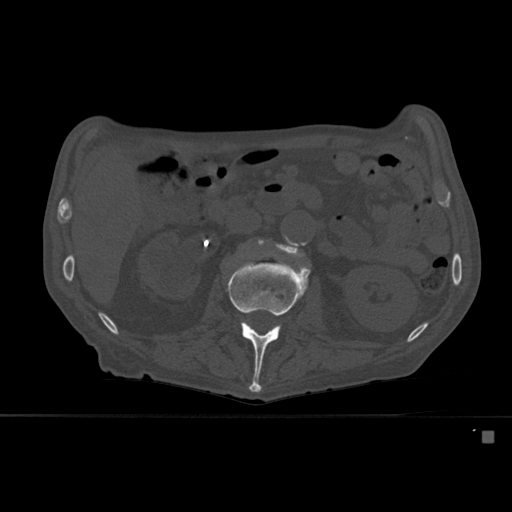
CT including the spine, one axial slice. Slice 231 of 527 in the series (ordered by position). Bone window (W 1800 / L 400 HU). 1.5 mm slice thickness. 512 × 512 image matrix, field of view 373 × 373 mm. Male patient, age 78 years. Case-level facts recorded for this patient, not image findings: primary cancer: prostate.
Structures marked on this image (semi-automatic segmentation, software-assisted and operator-edited):
- L2 vertebra: bounding box [x1, y1, x2, y2] px = [228, 261, 311, 393]
- L3 vertebra: [258, 235, 307, 262]